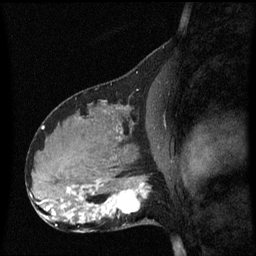
Breast MRI (dynamic contrast-enhanced), one sagittal slice; slice 31 of 60 in the series (ordered by position); dynamic contrast-enhanced series, image 2 of 3 at this slice position (ordered by acquisition); 1.5 T; TE 4.2 ms, TR 8.4 ms; 256 × 256 image matrix. Female patient, age 31 years. Case-level facts recorded for this patient, not image findings: setting: breast cancer imaged before/during neoadjuvant chemotherapy; receptor status: HR-positive, HER2-negative.
Outlined on this slice (semi-automatic segmentation, software-assisted and operator-edited):
- analysis volume of interest (the breast-tissue region the enhancement analysis was run in; not a lesion): bounding box <98,175,157,228> (left, top, right, bottom; pixels)
- tumour enhancement mask (voxels above the 70 % enhancement threshold inside the analysis volume of interest): <100,183,147,220>